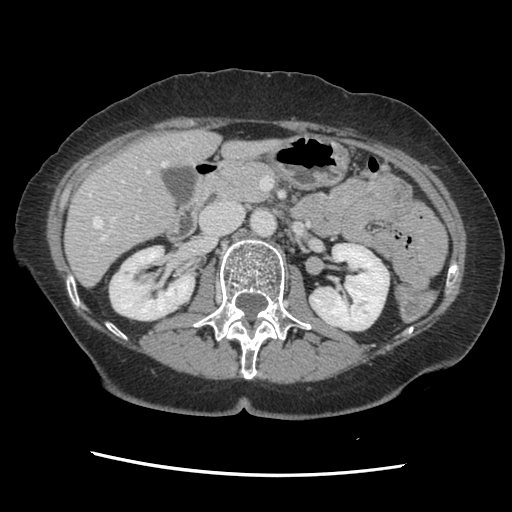
Contrast-enhanced abdominal CT, one axial slice. Position 67 of 141 along the scan axis. Soft-tissue window (W 400 / L 40 HU). 2.5 mm slice thickness. 512 × 512 image matrix, field of view 330 × 330 mm. Female patient, age 61 years. From the clinical record (not read from this slice): diagnosis: colorectal cancer liver metastases, imaged before liver resection; multiple liver metastases: no; largest metastasis: 2.4 cm.
Structures marked on this image (expert manual segmentation):
- hepatic veins: bounding box [x1, y1, x2, y2] px = [89, 161, 167, 228]
- liver: [66, 130, 277, 285]
- planned liver remnant (the part of the liver to remain after resection): [66, 130, 277, 285]
- portal vein (with intrahepatic branches): [100, 180, 141, 242]